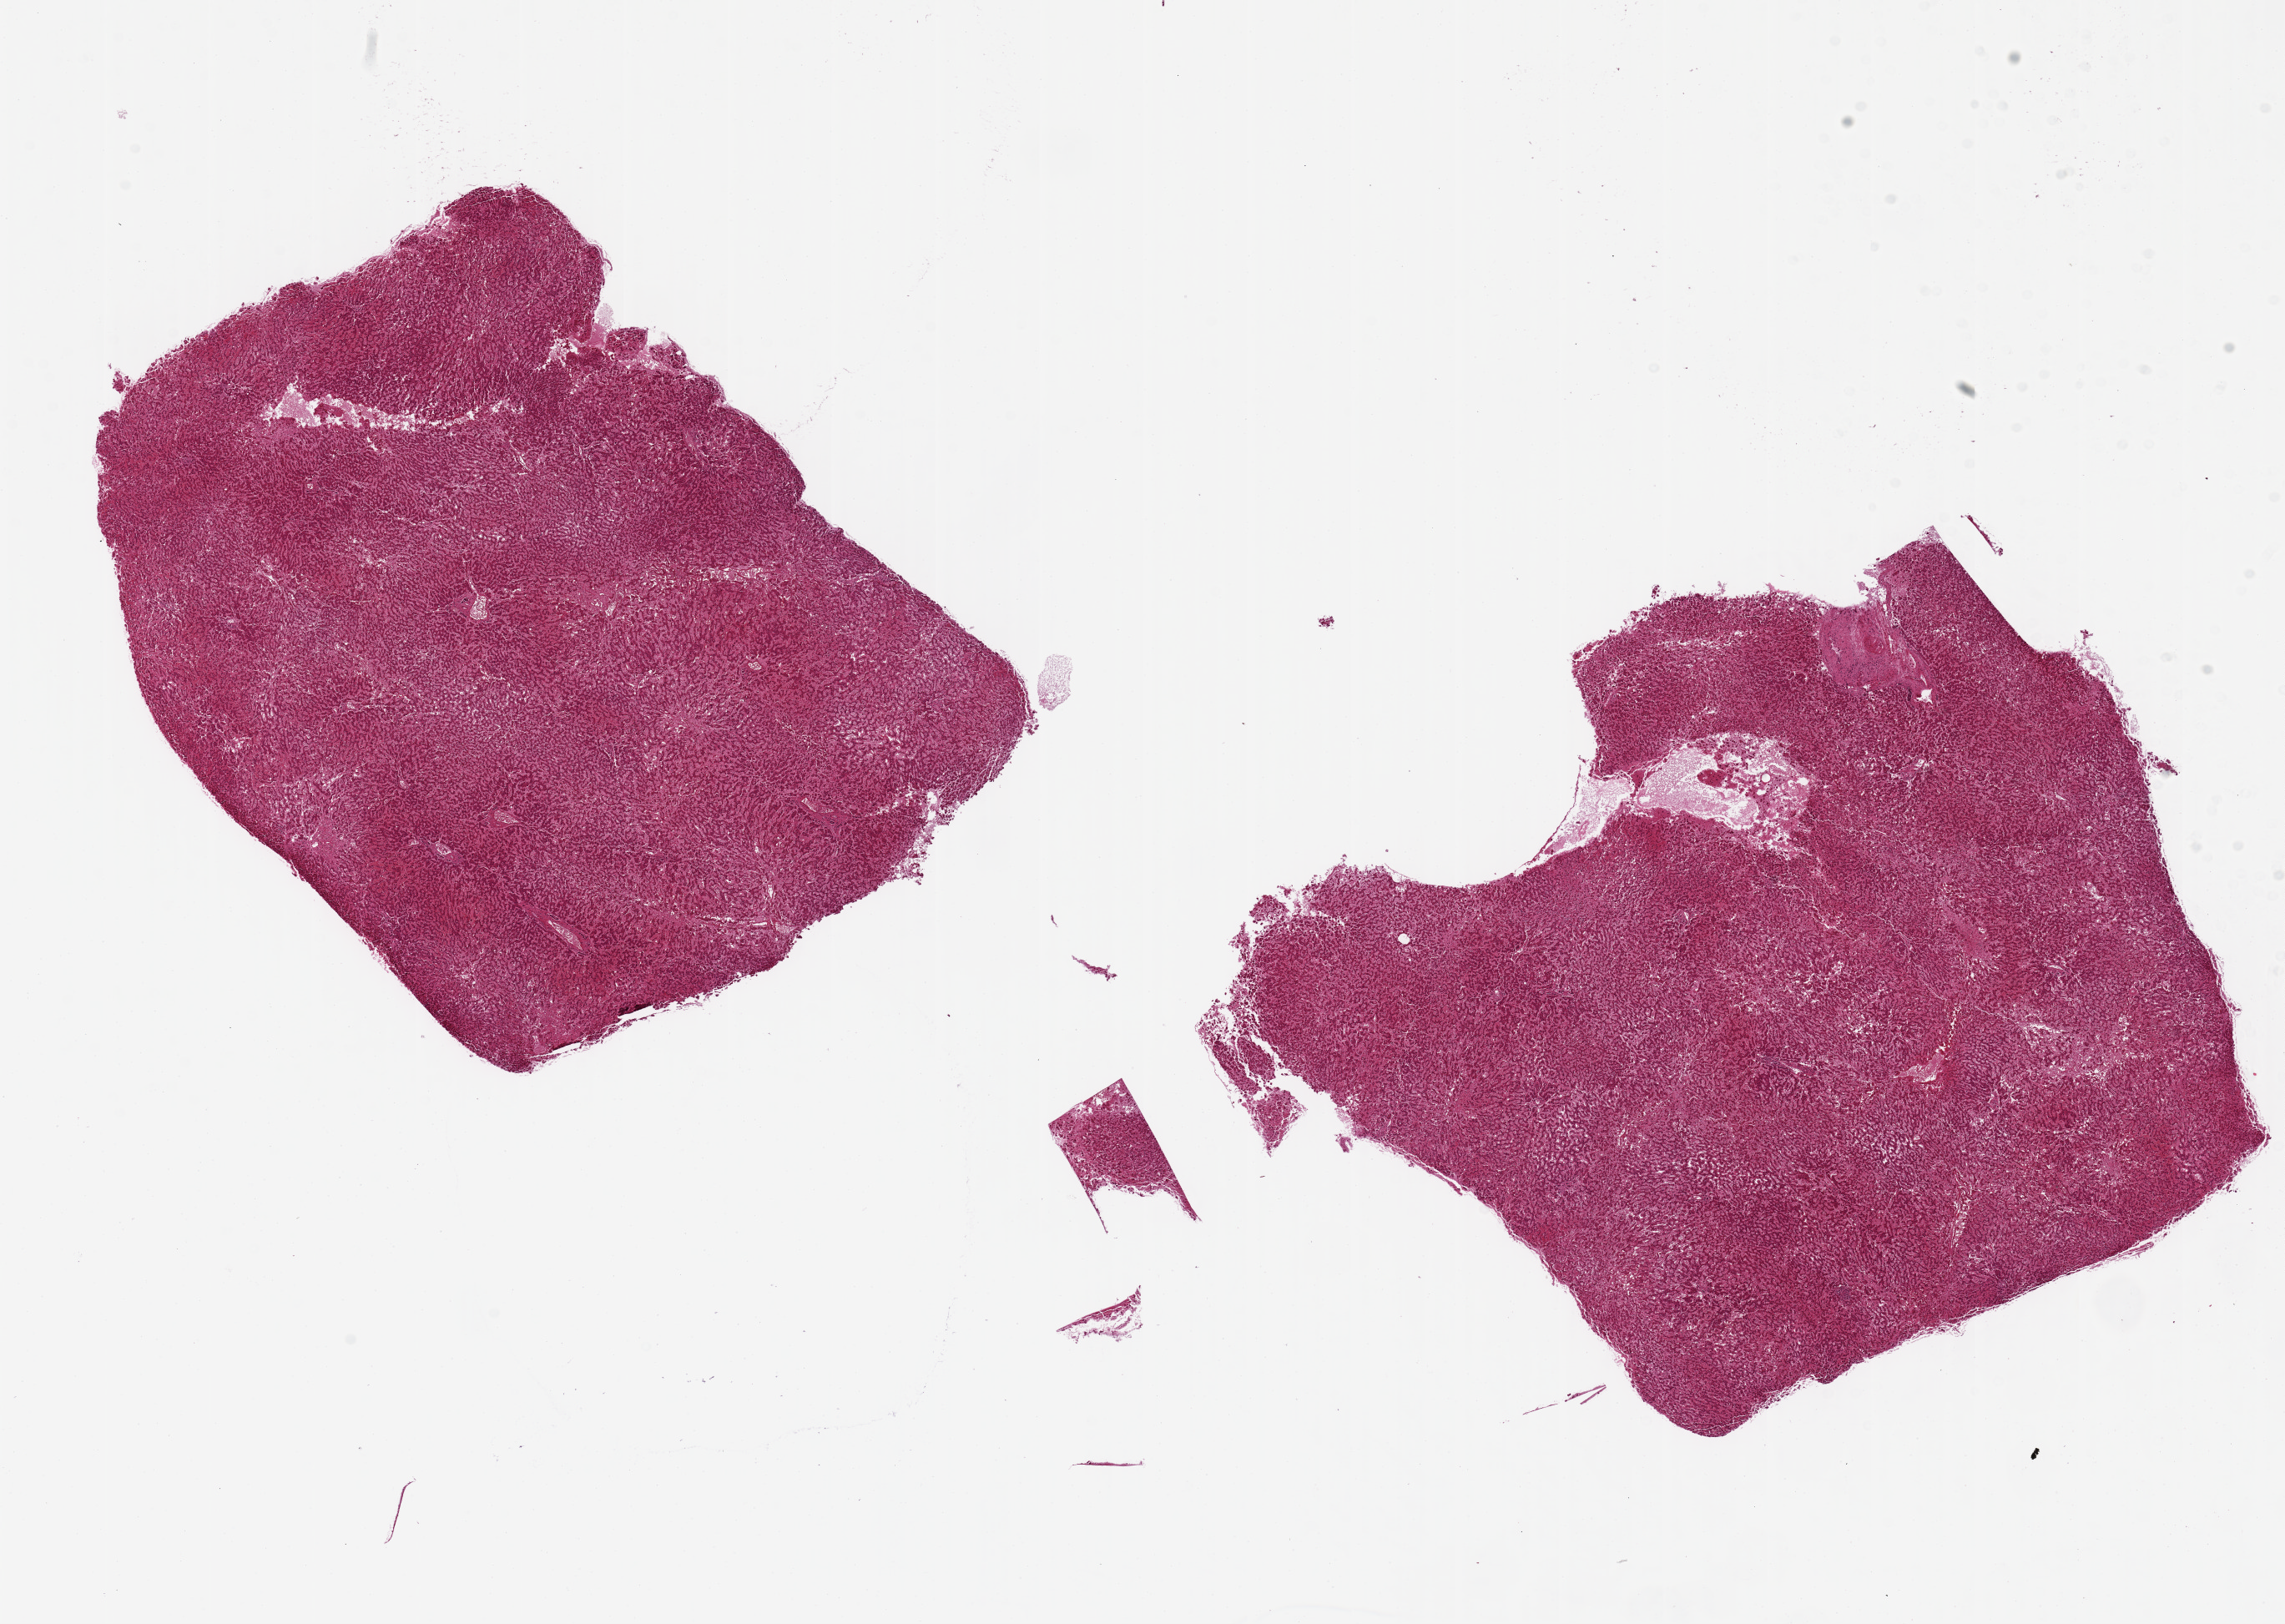
Hematoxylin and eosin (H&E) whole-slide image — shown as a low-resolution overview of the whole scanned area (about 21.7 x 15.4 mm, slide scanned at 20x). PAXgene-fixed paraffin-embedded (PFPE) section. Section of liver (target tissue). Tissue donor sample. Female donor.
- pathologist's review note for this sample: 2 pieces, 8x6 & 9x7.5mm; congested and autolyzed